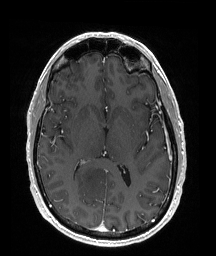
Brain MRI from a brain-tumour surgery series, one axial slice. Position 92 of 176 along the scan axis. T1-weighted post-contrast. 216 × 256 image matrix, field of view 211 × 250 mm. From the clinical record (not read from this slice): histopathology: Oligodendroglioma; WHO grade: 2; IDH mutation: yes; tumour location: Right Parietal.
Structures marked on this image (outlined manually by an expert reader):
- tumour: bounding box <71,163,106,199> (left, top, right, bottom; pixels)